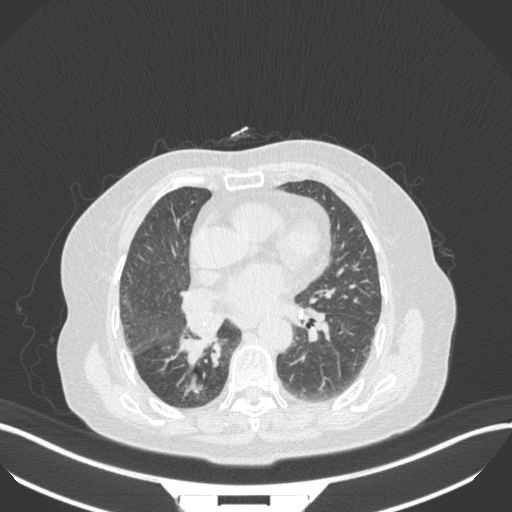
Chest CT, one axial slice. Position 150 of 329 along the scan axis. Reconstruction kernel B31f. Lung window (W 1500 / L -600 HU). 1 mm slice thickness. 512 × 512 image matrix, field of view 400 × 400 mm. Female patient, age 75 years. Case-level facts recorded for this patient, not image findings: clinical TNM (as recorded): T1b N0 M1a.
Outlined on this slice (rectangle marked by the reading radiologist):
- lung tumour (recorded histology: squamous cell carcinoma): bounding box (x1, y1, x2, y2) in pixels: (178, 334, 213, 365)